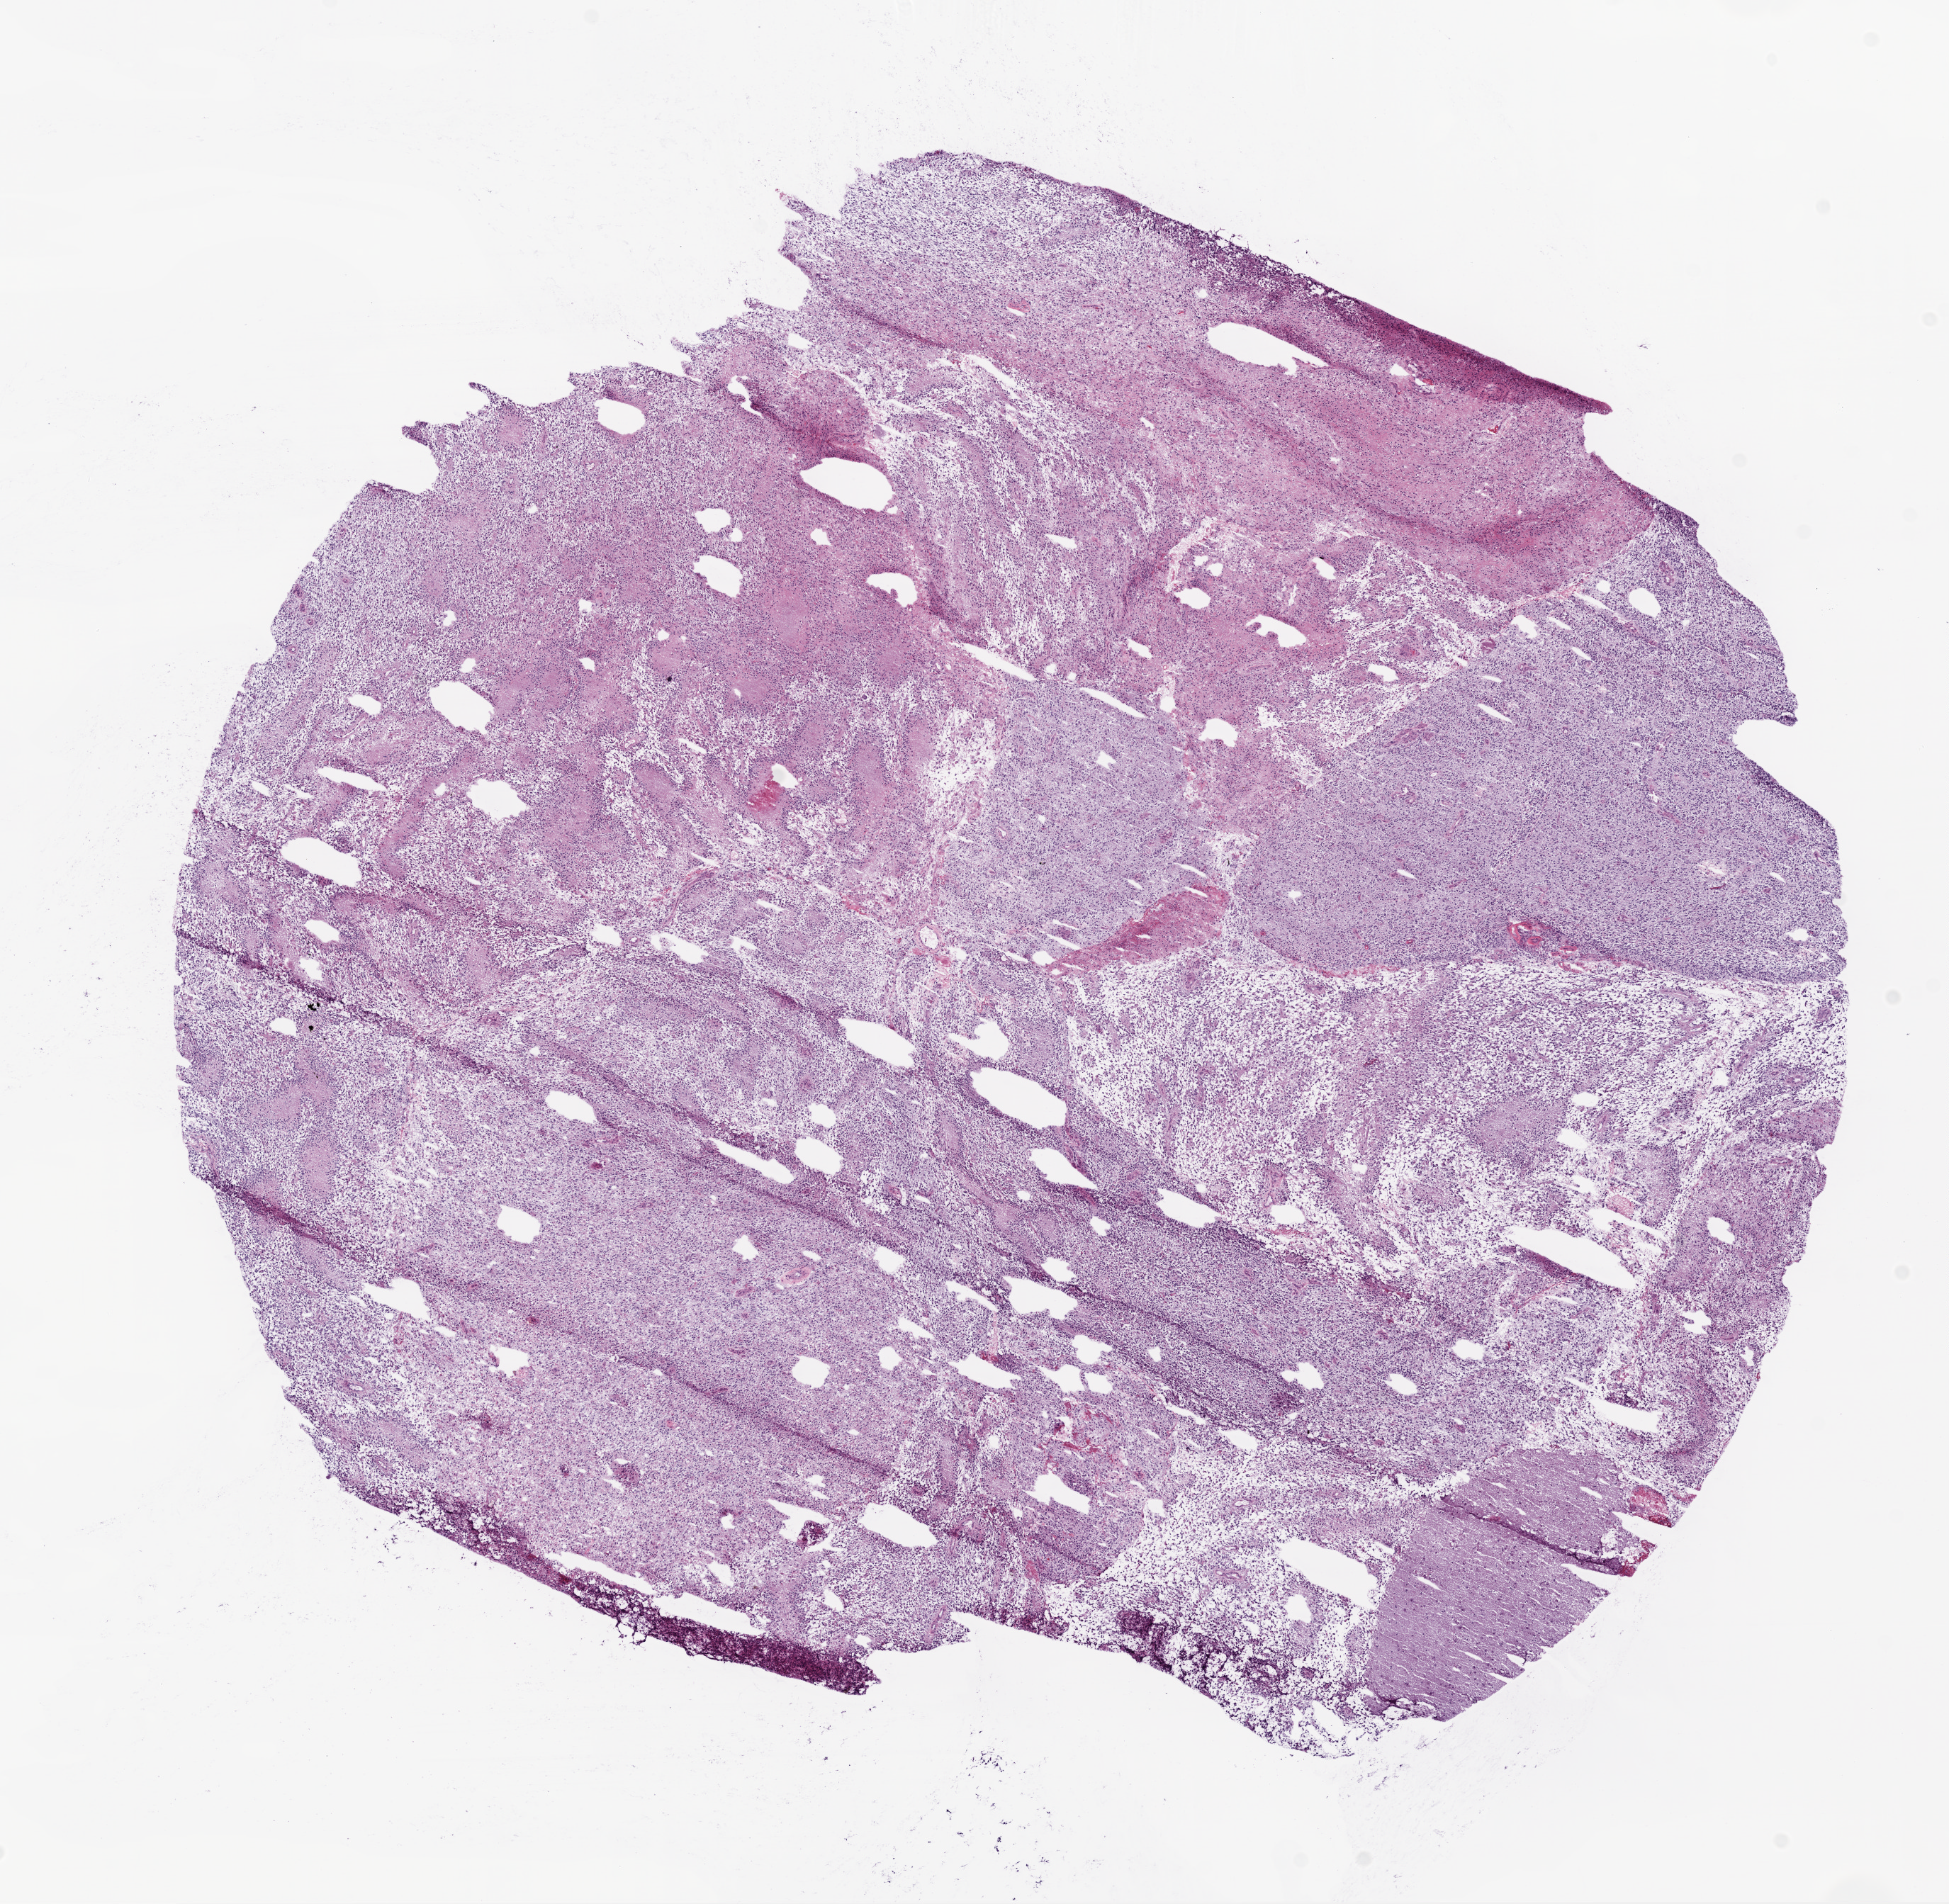
Whole-slide histology image, H&E, whole scanned area (about 11.0 x 10.8 mm, slide scanned at 20x) shown as a low-resolution overview; frozen section from the bottom of the tissue portion; sample: primary tumour, brain. Patient: male, age at initial diagnosis 75 years. Pathologist review of this section (percent, as recorded): tumour cells 65%, tumour nuclei 80%, normal cells 0%, stromal cells 0%, necrosis 35%.
• diagnosis: Glioblastoma